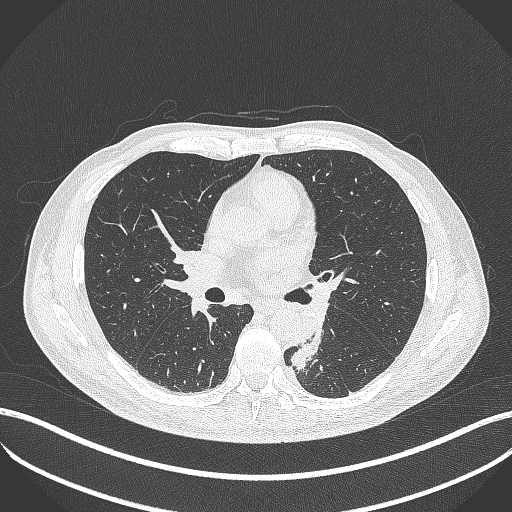
Chest CT, one axial slice. Position 223 of 451 along the scan axis. Lung window (W 1500 / L -600 HU). 1 mm slice thickness. 512 × 512 image matrix, field of view 400 × 400 mm. Patient: male, 72 years. From the clinical record (not read from this slice): clinical TNM (as recorded): T2b N0 M1.
Structures marked on this image (rectangle marked by the reading radiologist):
- lung tumour (recorded histology: adenocarcinoma): box from (x=283, y=329) to (x=326, y=371) px